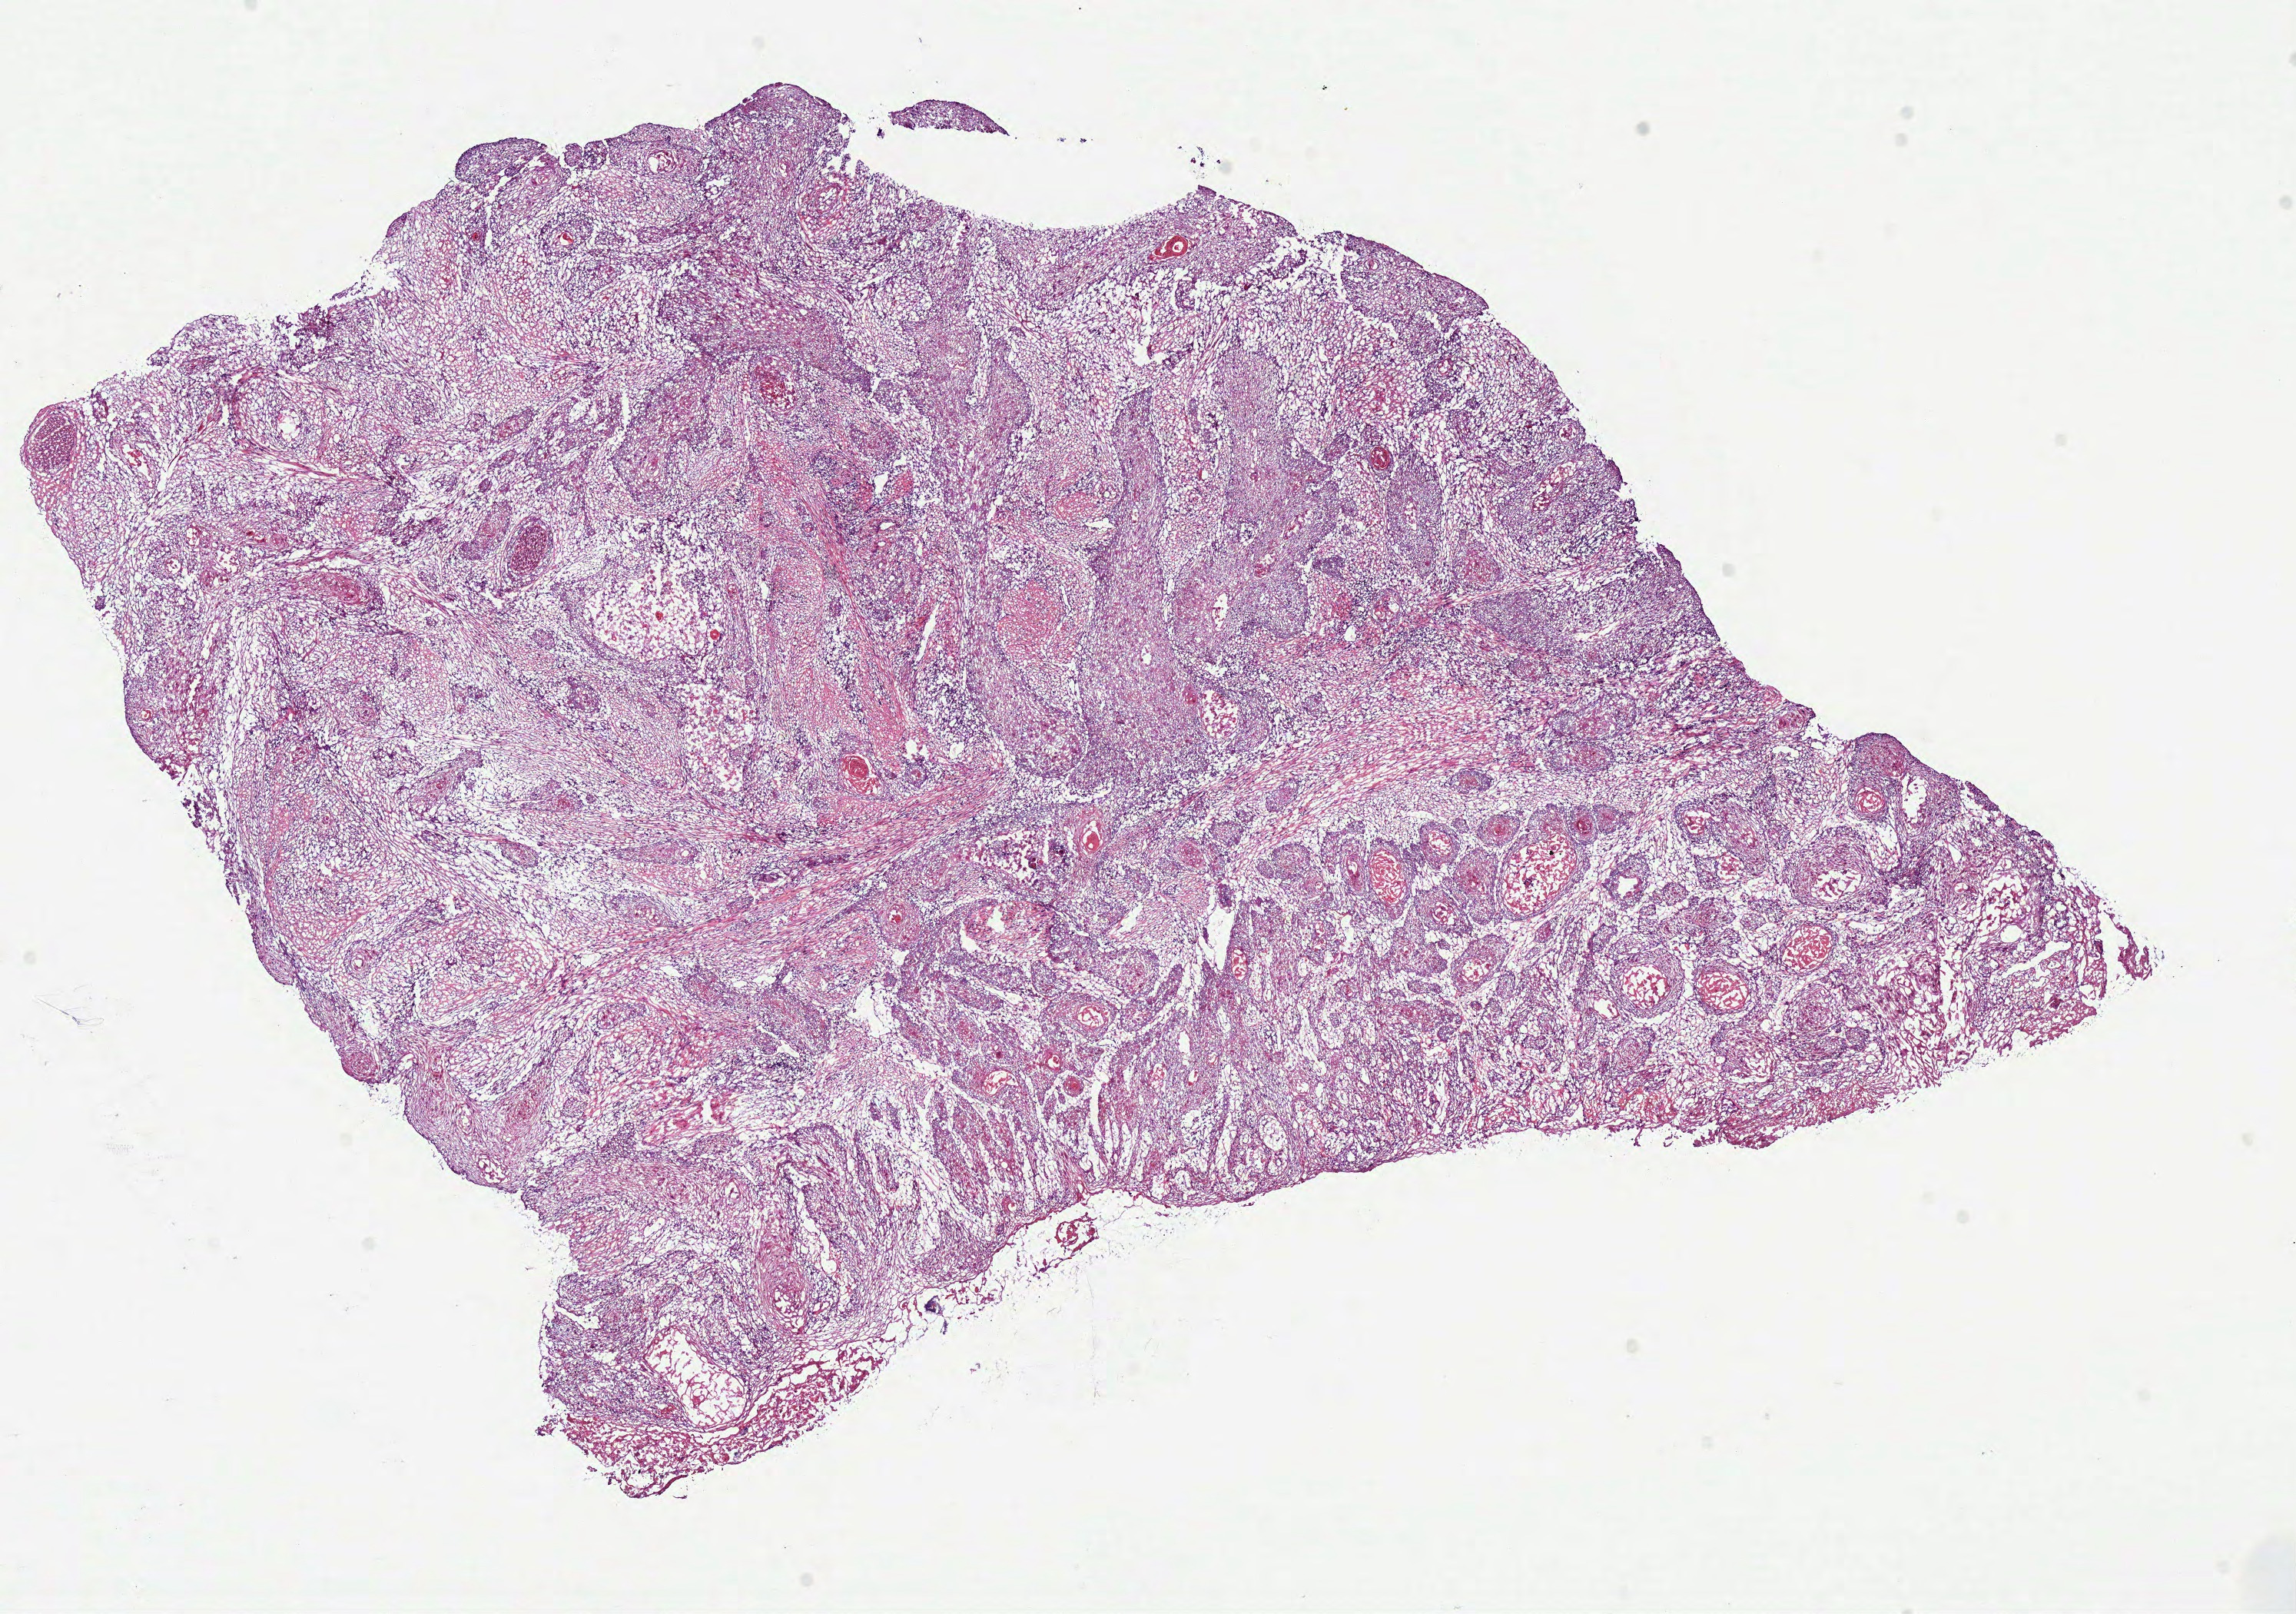
Digitized H&E-stained tissue section (whole slide), low-resolution overview of the scanned area, about 11.7 x 8.3 mm. Frozen section. Primary tumour sample from the head and neck. Patient: male, age at initial diagnosis 73 years. Histologic grade: G2 (moderately differentiated). Composition of this section per pathologist review: tumour cells 83%, tumour nuclei 80%, normal cells 0%, stromal cells 15%, necrosis 2%.
Lymph nodes positive (case pathology): 1 of 49 examined. Pathologic diagnosis: Squamous cell carcinoma, NOS (tongue, NOS). Laterality: right.